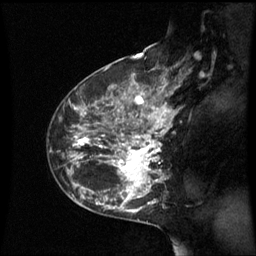
Breast MRI (dynamic contrast-enhanced), one sagittal slice. Slice 38 of 60 in the series (ordered by position). Dynamic contrast-enhanced series, image 2 of 3 at this slice position (ordered by acquisition). 1.5 T. TE 4.2 ms, TR 8.9 ms. 2.4 mm slice thickness. 256 × 256 image matrix. Patient: female, 42 years. Case-level facts recorded for this patient, not image findings: setting: breast cancer imaged before/during neoadjuvant chemotherapy; receptor status: HER2-positive.
Annotated regions visible in this slice (semi-automatically segmented with operator editing):
- analysis volume of interest (the breast-tissue region the enhancement analysis was run in; not a lesion): bounding box <62,93,171,210> (left, top, right, bottom; pixels)
- tumour enhancement mask (voxels above the 70 % enhancement threshold inside the analysis volume of interest): <76,93,171,209>